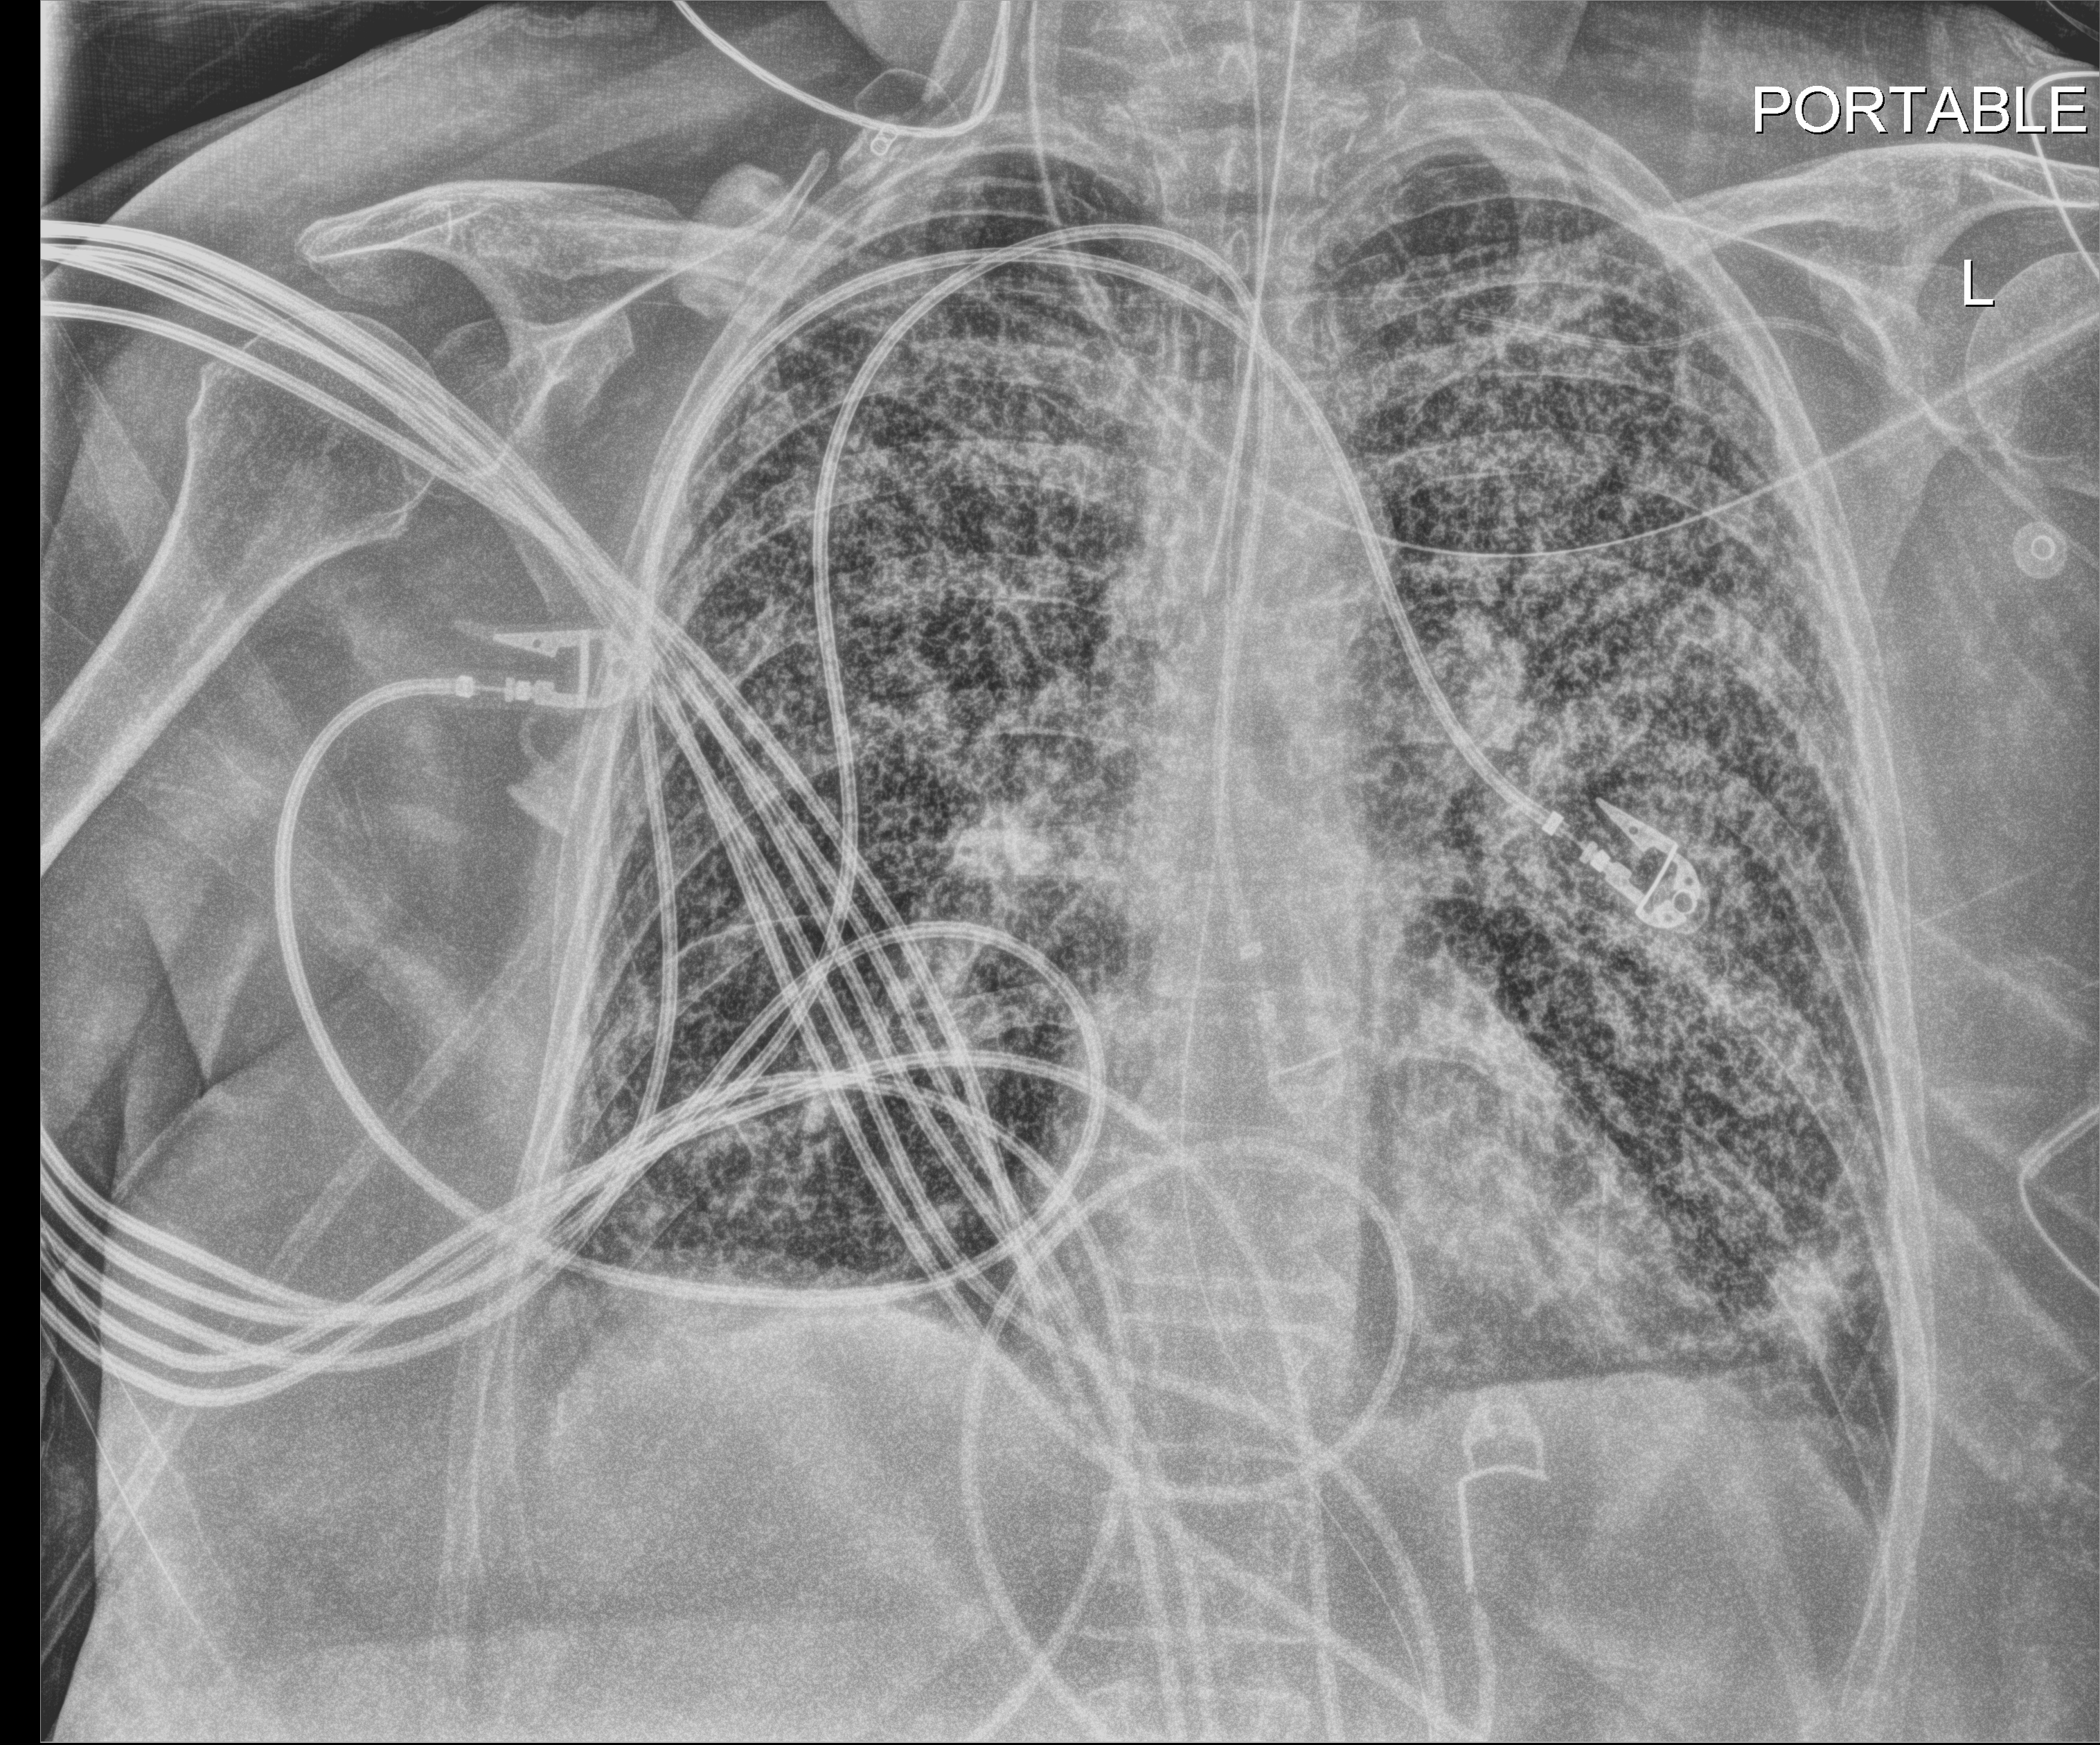
Chest radiograph. Female patient hospitalised with COVID-19, age 60–74 years.
From the hospital-stay record, not from the radiograph (when in the stay this image was taken is not recorded): mechanically ventilated during this hospital stay: yes; admitted to intensive care during this hospital stay: yes.